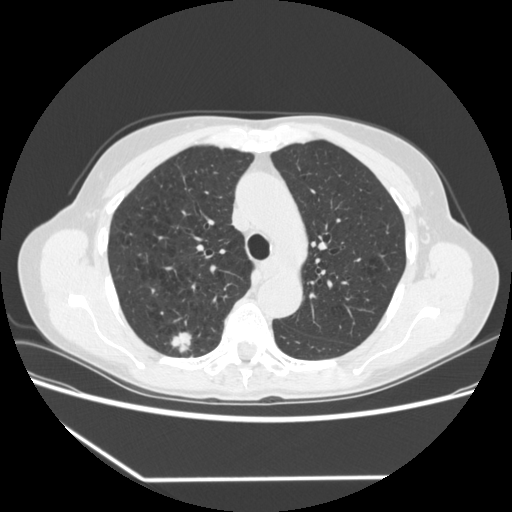
Low-dose screening chest CT, one axial slice; position 238 of 323 along the scan axis; reconstruction kernel STANDARD; lung window (W 1500 / L -600 HU); 1.25 mm slice thickness; 512 × 512 image matrix.
Outlined on this slice (manually delineated by an expert):
- lesion 1 (tumor, upper lobe of right lung): bounding box [x1, y1, x2, y2] px = [171, 332, 192, 353]